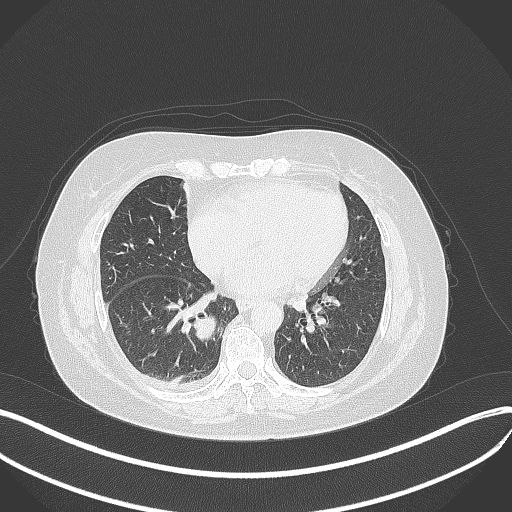
Chest CT, one axial slice. Reconstruction kernel B70f. 120 kVp. Lung window (W 1500 / L -600 HU). 1 mm slice thickness. 512 × 512 image matrix, field of view 400 × 400 mm. Female patient, age 56 years. Case-level facts recorded for this patient, not image findings: clinical TNM (as recorded): T2b N1 M0; histopathological grade: G3.
Structures marked on this image (rectangle marked by the reading radiologist):
- lung tumour (recorded histology: small cell carcinoma): bounding box <187,304,220,343> (left, top, right, bottom; pixels)